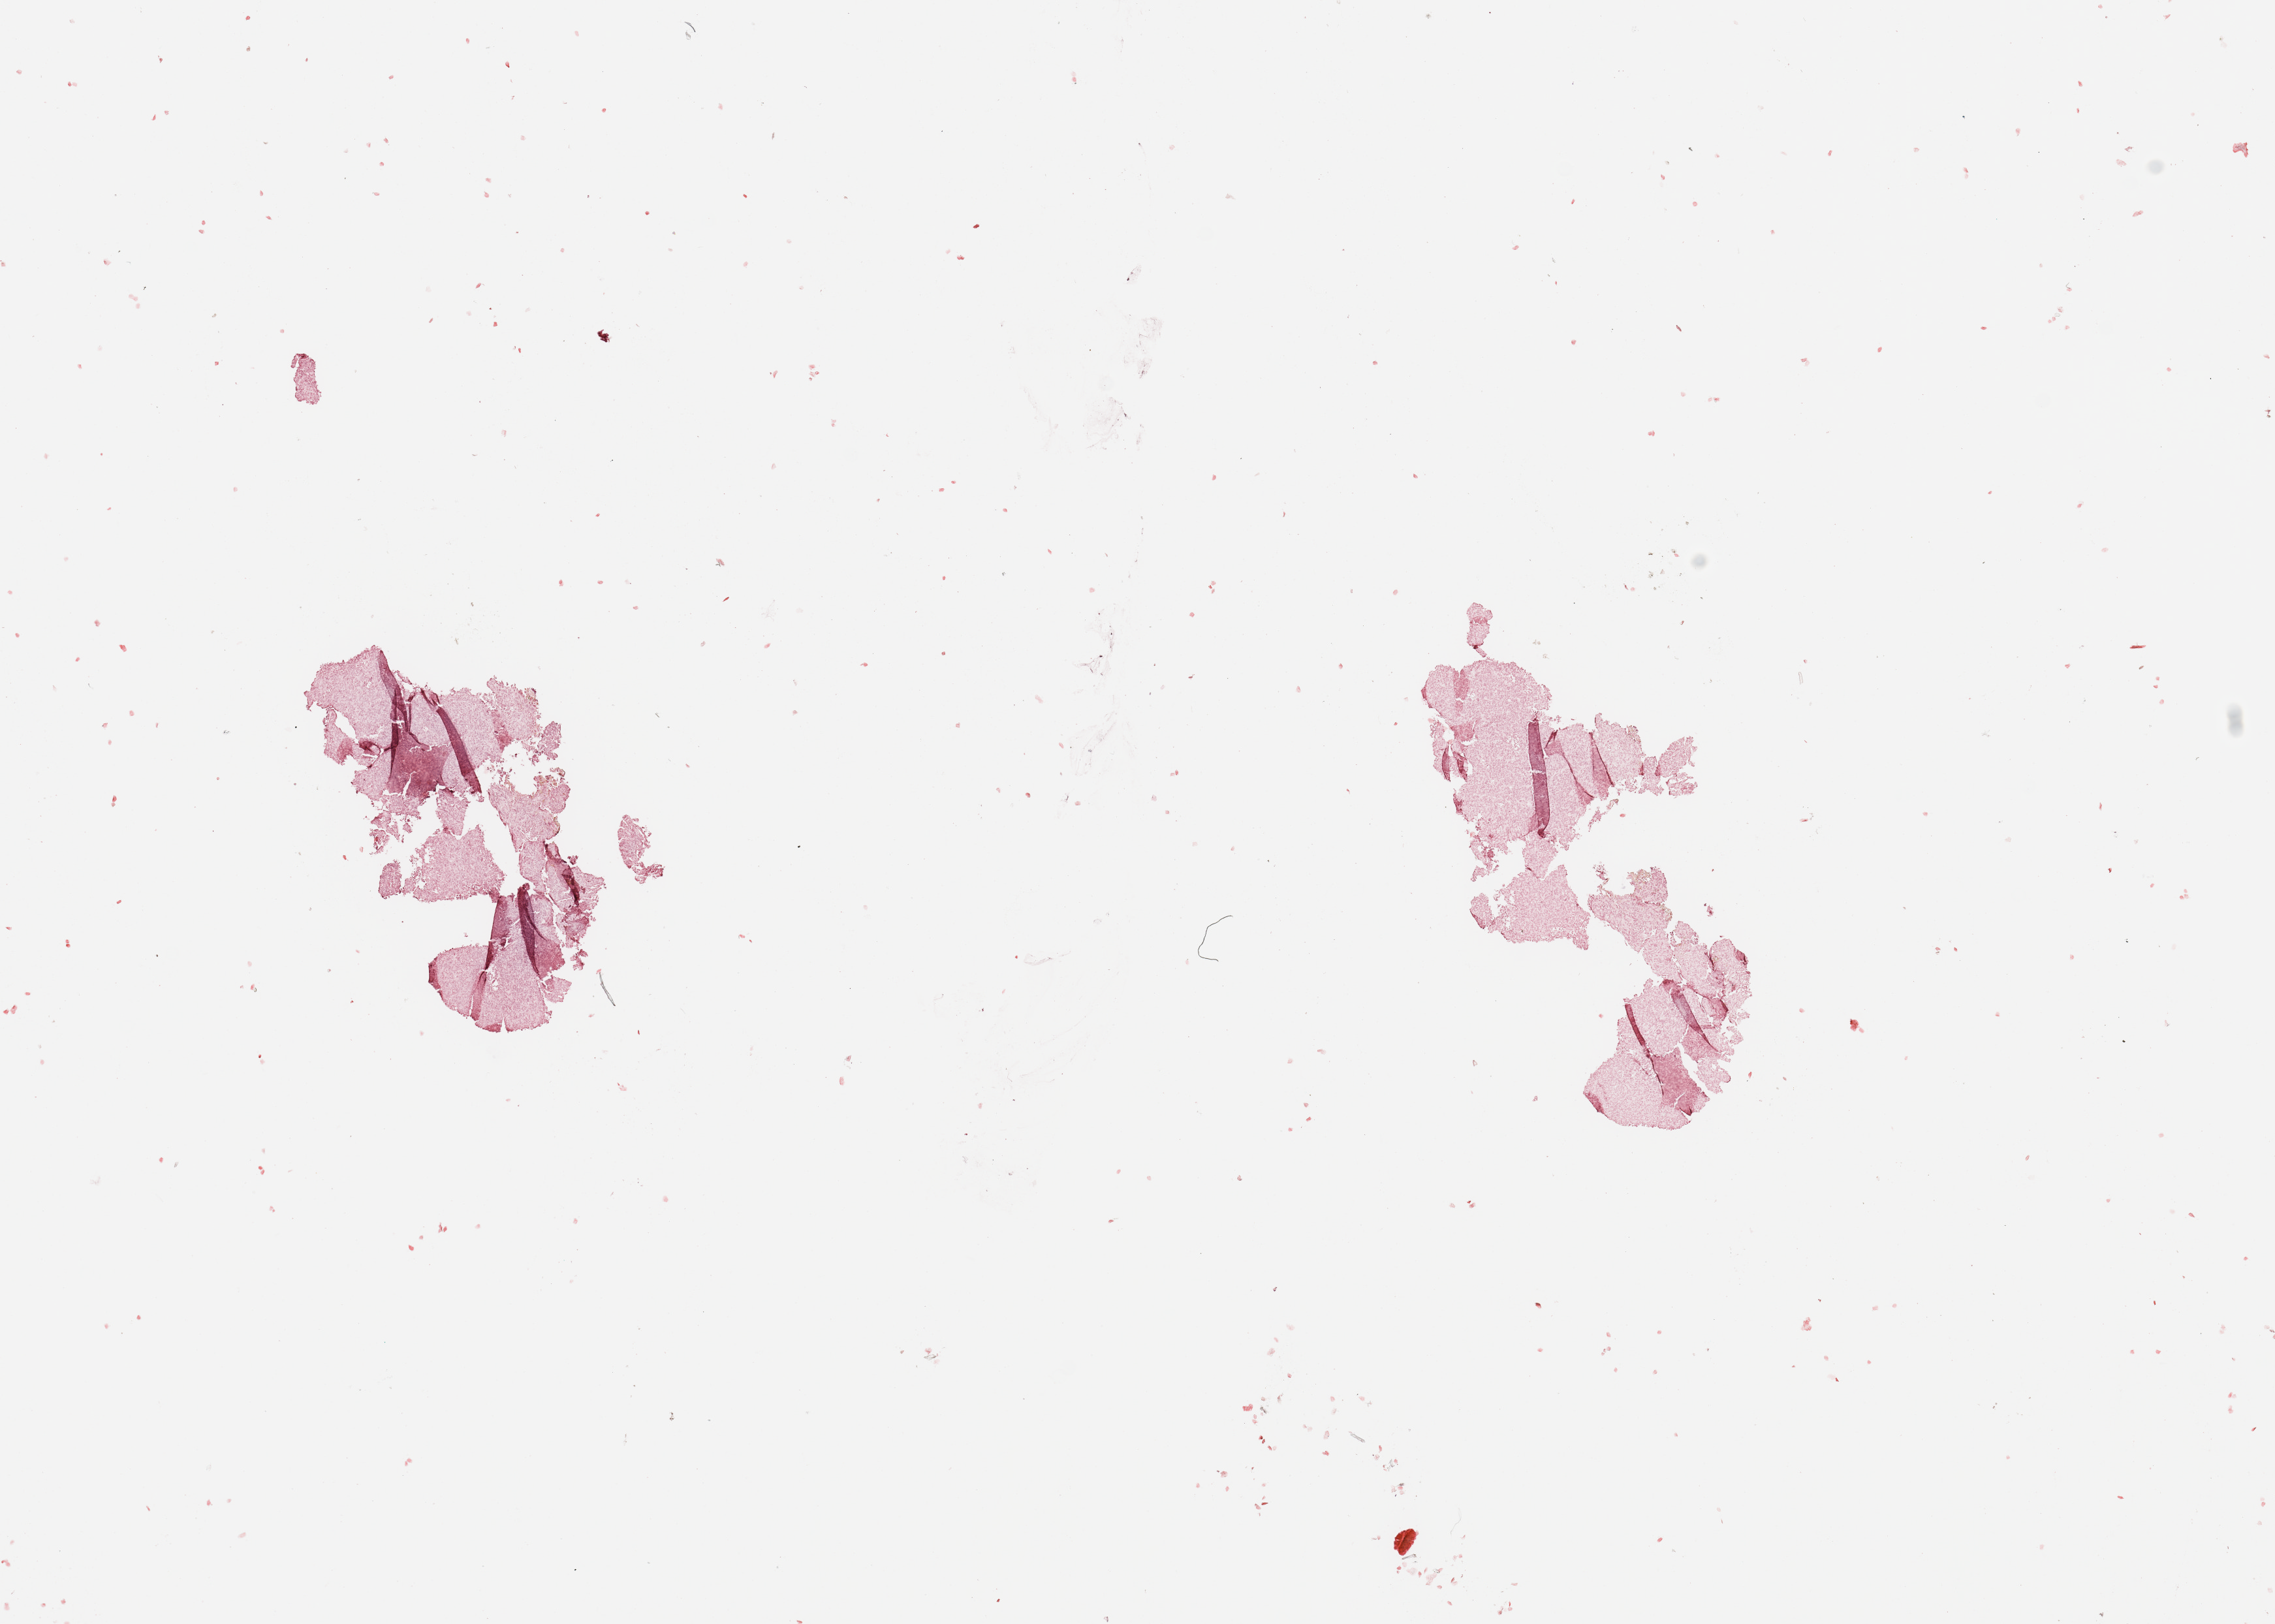
Hematoxylin and eosin (H&E) stained whole-slide image — a low-resolution overview of the entire scanned area, about 13.8 x 9.8 mm. 59-year-old female patient.
Patient diagnosis (cohort enrolment): sarcoma (site not recorded at cohort level).